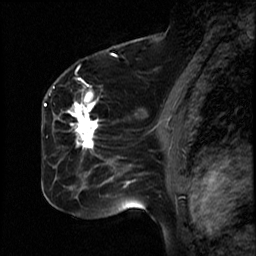
Breast MRI (dynamic contrast-enhanced), one sagittal slice; slice 31 of 50 in the series (ordered by position); dynamic contrast-enhanced study with each time point stored as its own series, time point 2 of 4 at this slice position (early post-contrast, ordered by acquisition time); 1.5 T; TE 4.2 ms, TR 18.5 ms; 3 mm slice thickness; 256 × 256 image matrix, field of view 200 × 200 mm. Female patient, age 44 years. Case-level facts recorded for this patient, not image findings: setting: breast cancer imaged before/during neoadjuvant chemotherapy; receptor status: HR-positive, HER2-negative.
Annotated regions visible in this slice (semi-automatic segmentation, software-assisted and operator-edited):
- analysis volume of interest (the breast-tissue region the enhancement analysis was run in; not a lesion): bounding box <59,80,114,206> (left, top, right, bottom; pixels)
- tumour enhancement mask (voxels above the 100 % enhancement threshold inside the analysis volume of interest): <67,101,100,149>